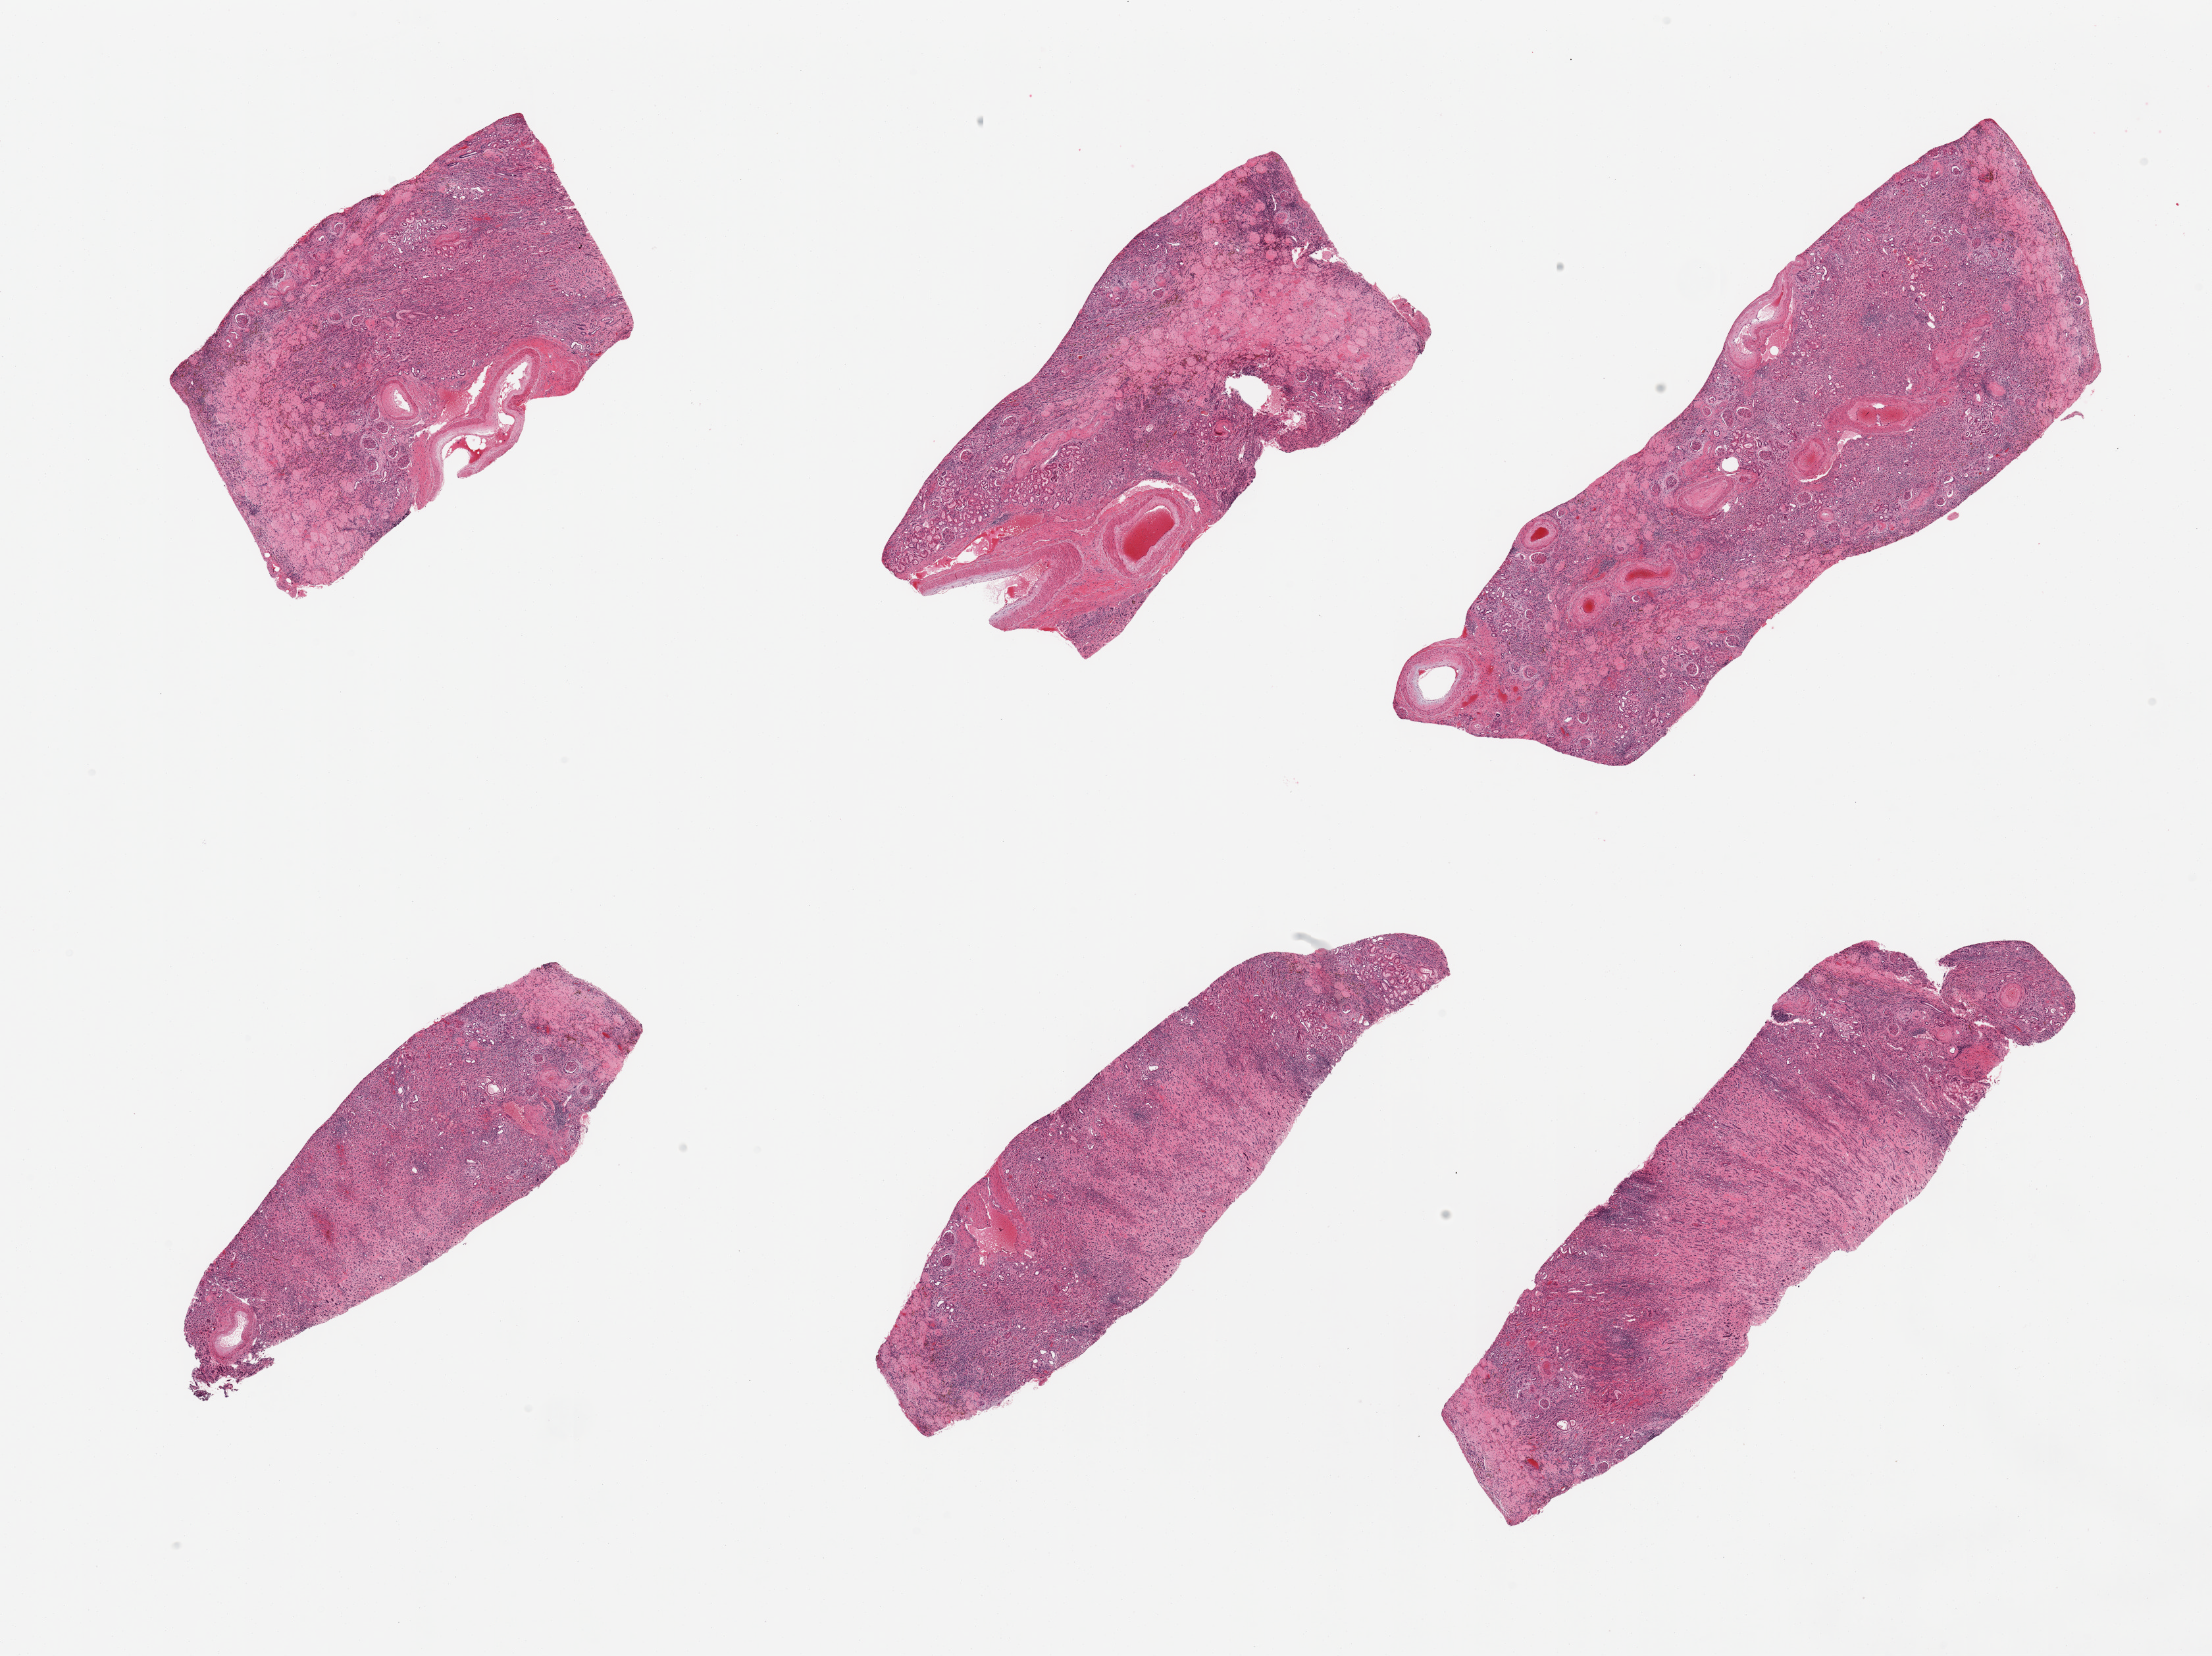
Whole-slide image, hematoxylin and eosin (H&E) stain — low-resolution overview of the scanned area, about 26.6 x 19.9 mm (slide scanned at 20x). PAXgene-fixed, paraffin-embedded tissue. Target tissue: renal cortex. Donor tissue sample. Donor: female.
Reviewer comment on this tissue sample: 6 pieces; includes medulla, cortex is largely sclerotic, numerous hemosiderin-laden cells.